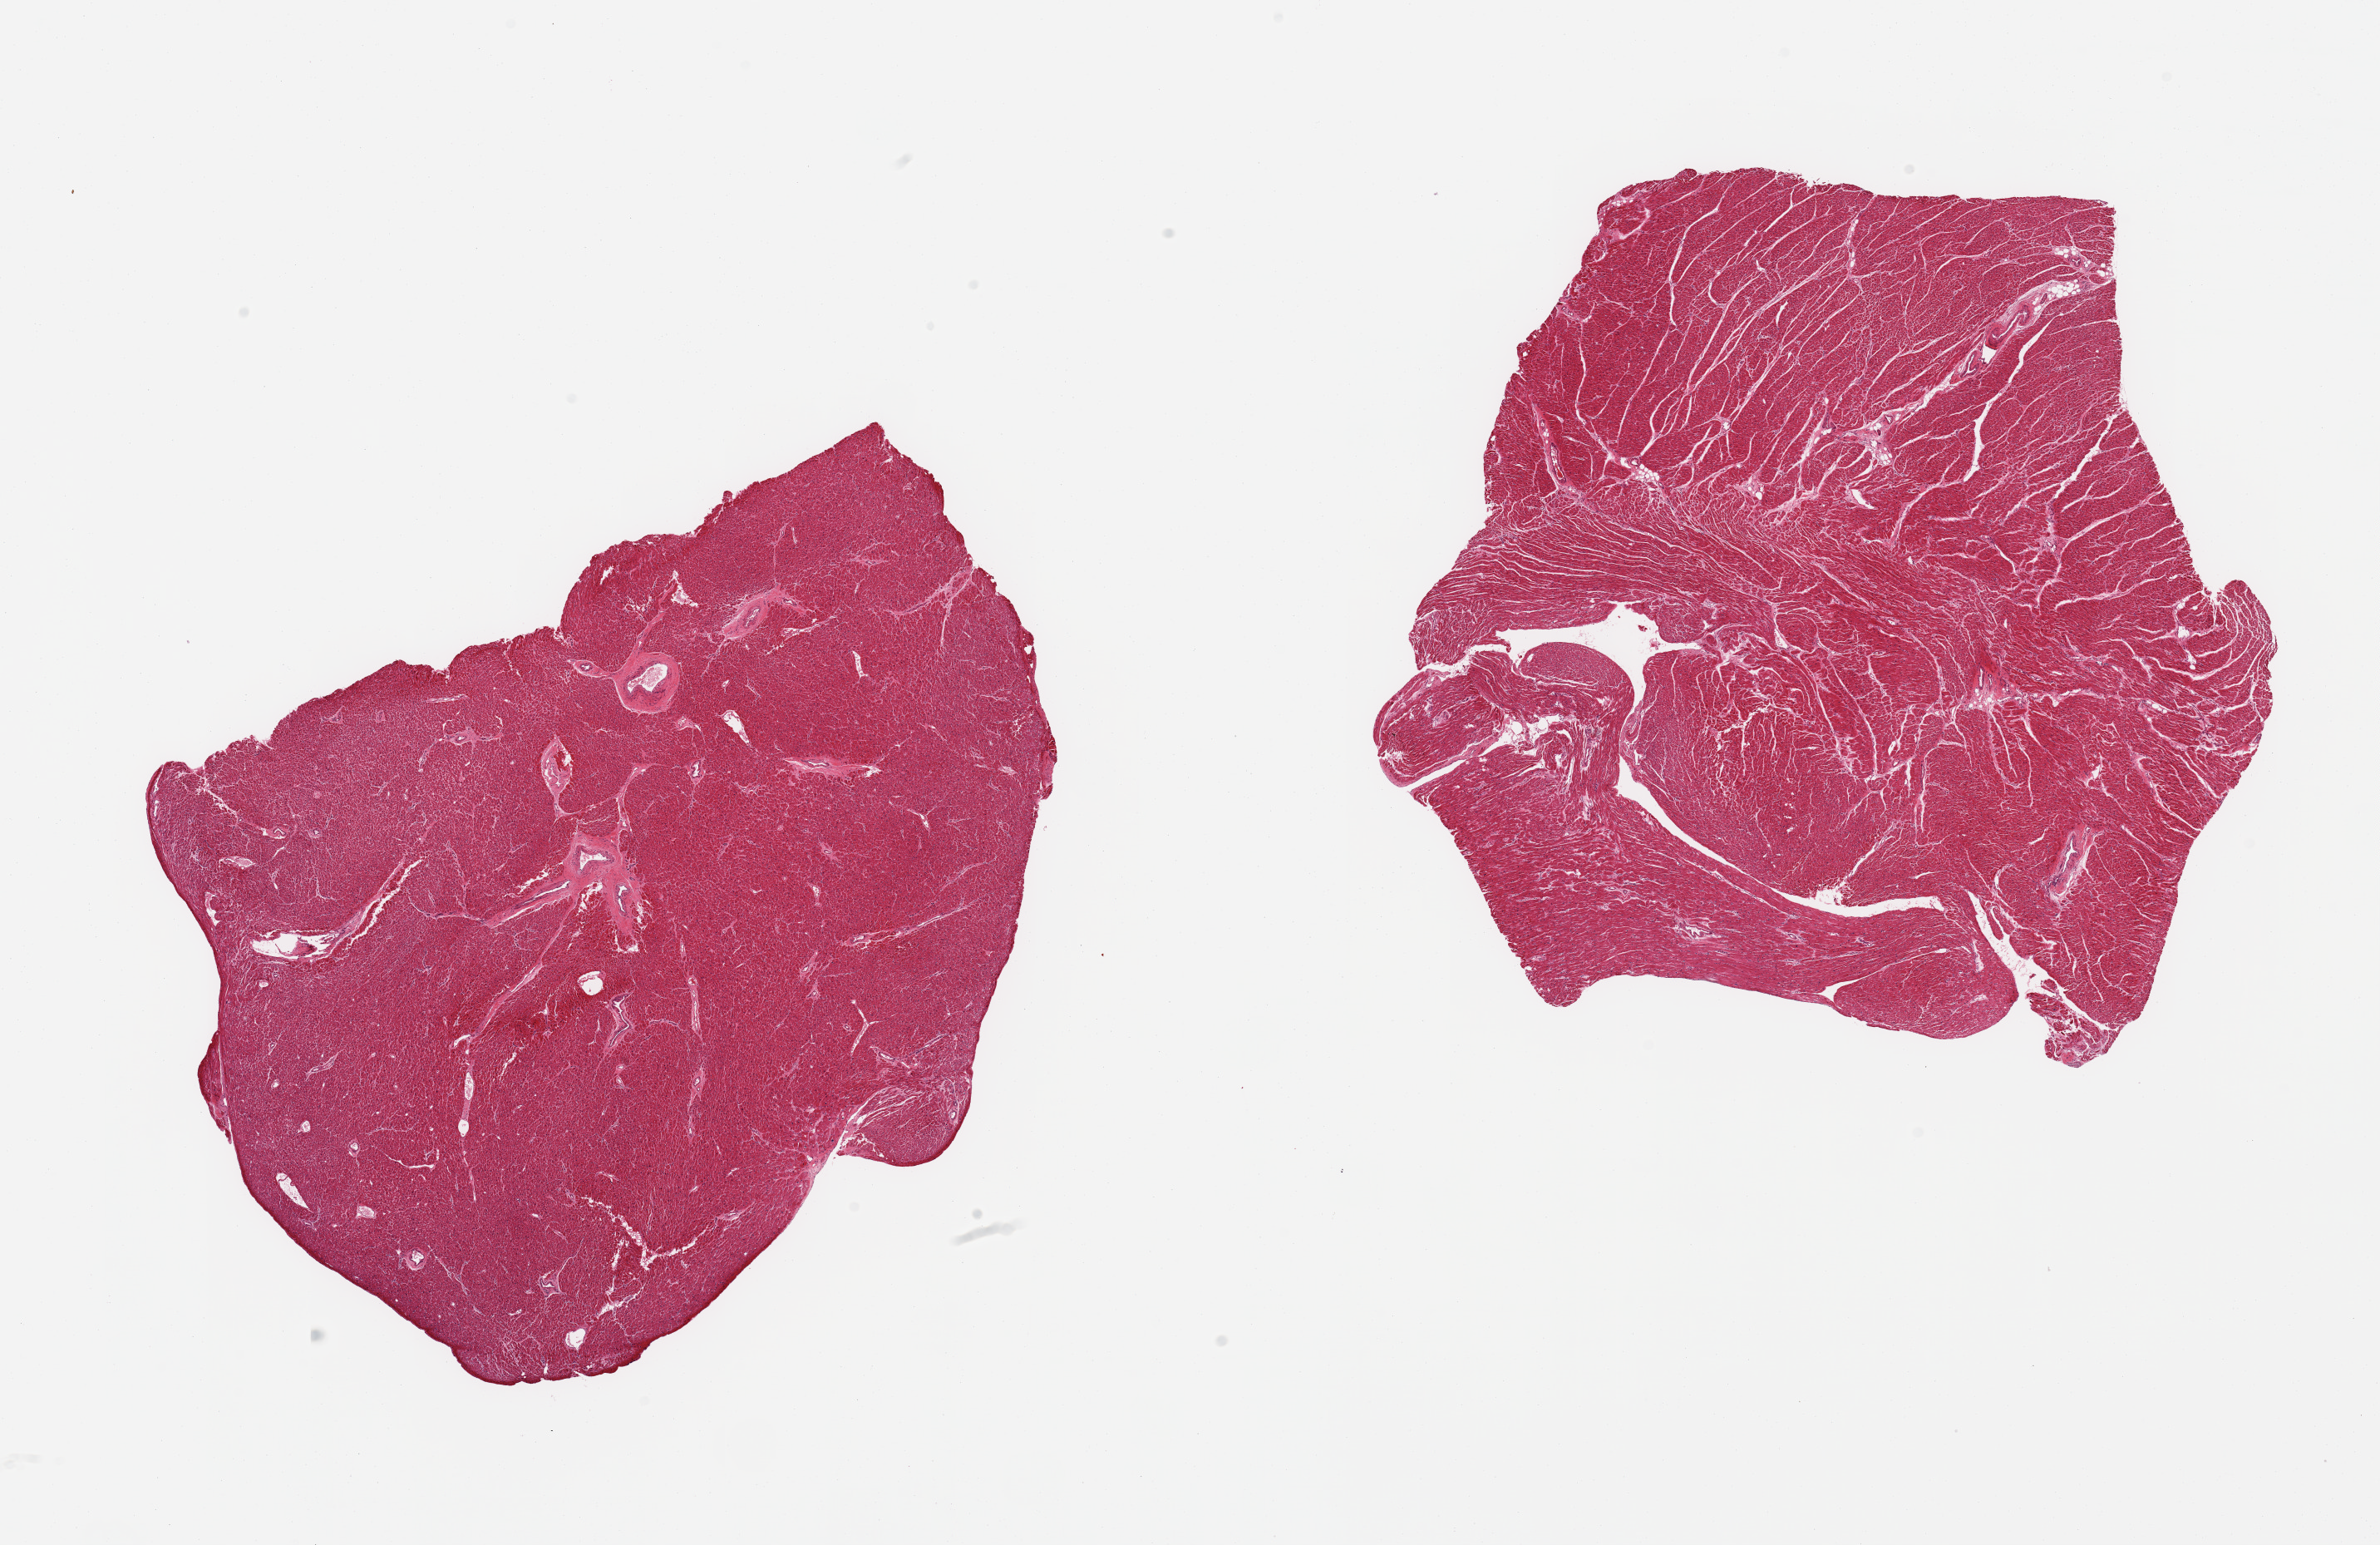
Hematoxylin and eosin (H&E) whole-slide image, low-resolution overview of the scanned area, about 22.6 x 14.7 mm; PAXgene-fixed paraffin-embedded (PFPE) section; section of heart (target tissue); donor tissue sample. Female donor.
Reviewer comment on this tissue sample: 2 pieces.